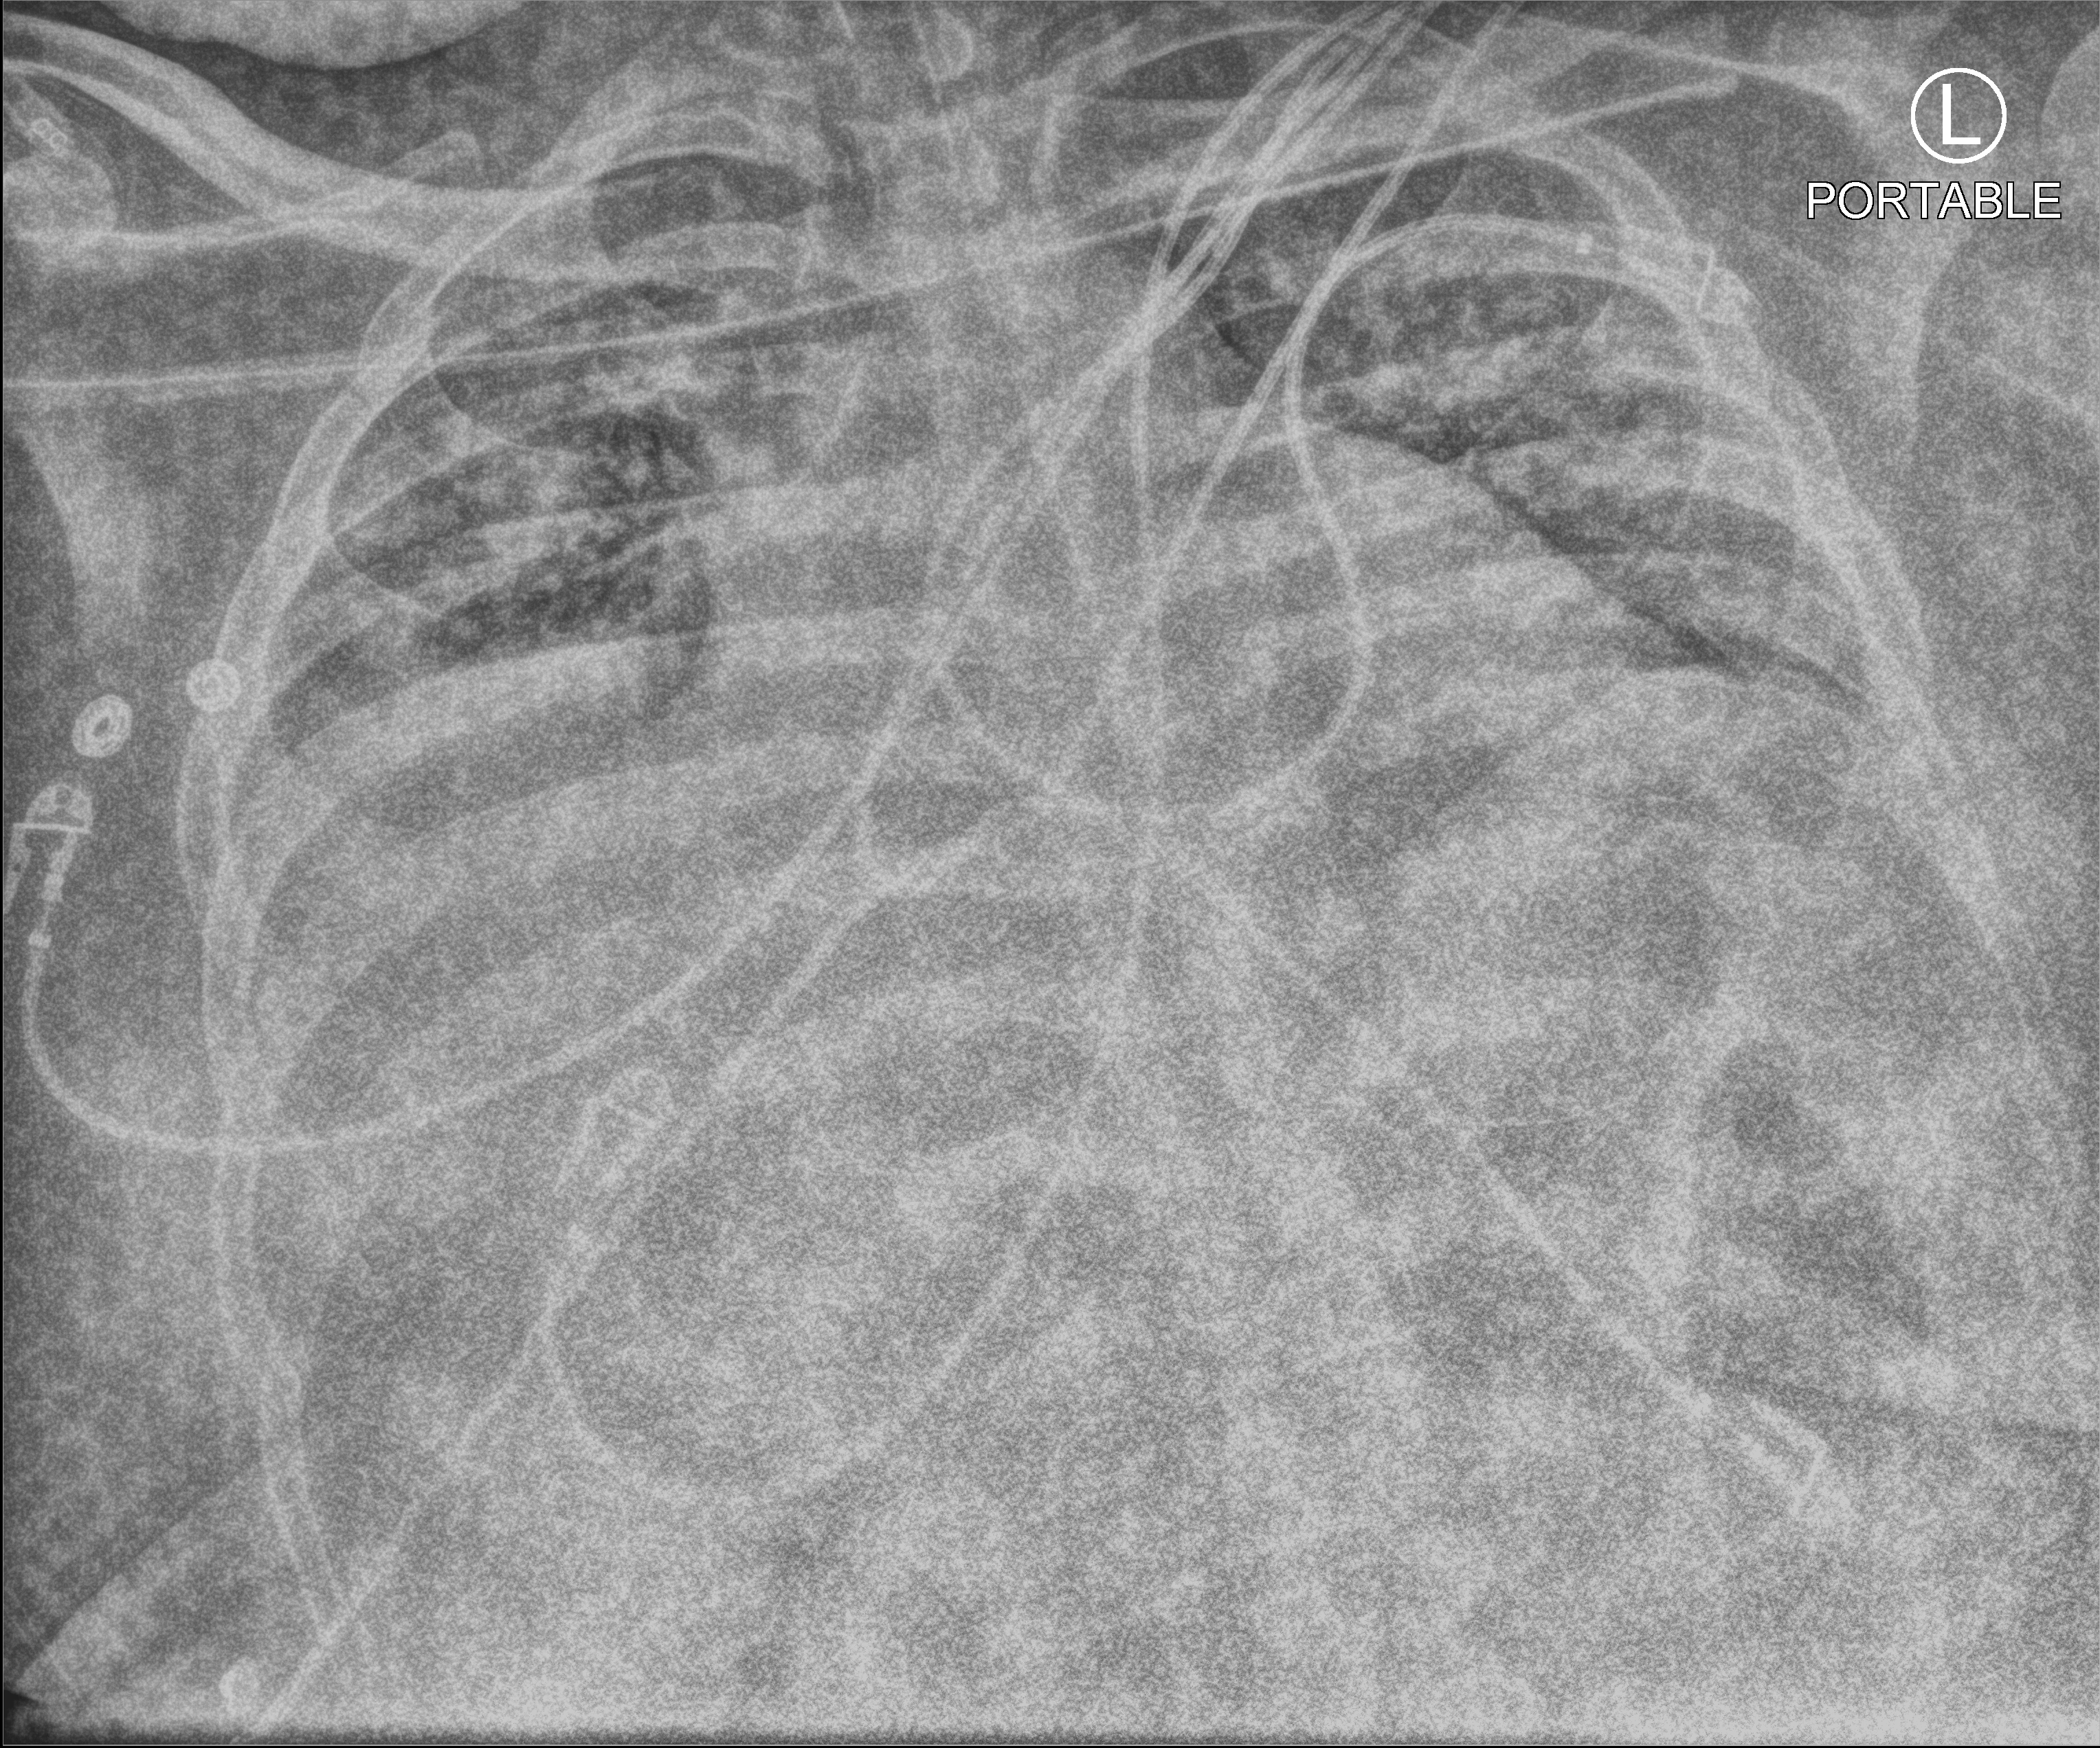
Portable chest radiograph, anteroposterior (AP) projection. Male patient hospitalised with COVID-19, age 18–59 years.
Admission-level facts for this patient (not findings on this image; timing relative to this image not recorded): length of hospital stay: 69 days.